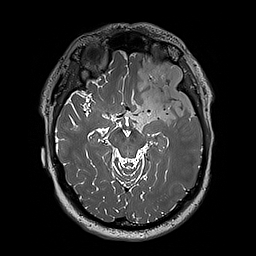
Brain MRI from a brain-tumour surgery series, one axial slice. Slice 126 of 192 in the series (ordered by position). 1 mm slice thickness. 256 × 256 image matrix. From the clinical record (not read from this slice): histopathology: Oligodendroglioma; WHO grade: 3; IDH mutation: yes.
Annotated regions visible in this slice (expert manual segmentation):
- tumour: box from (x=124, y=58) to (x=197, y=130) px